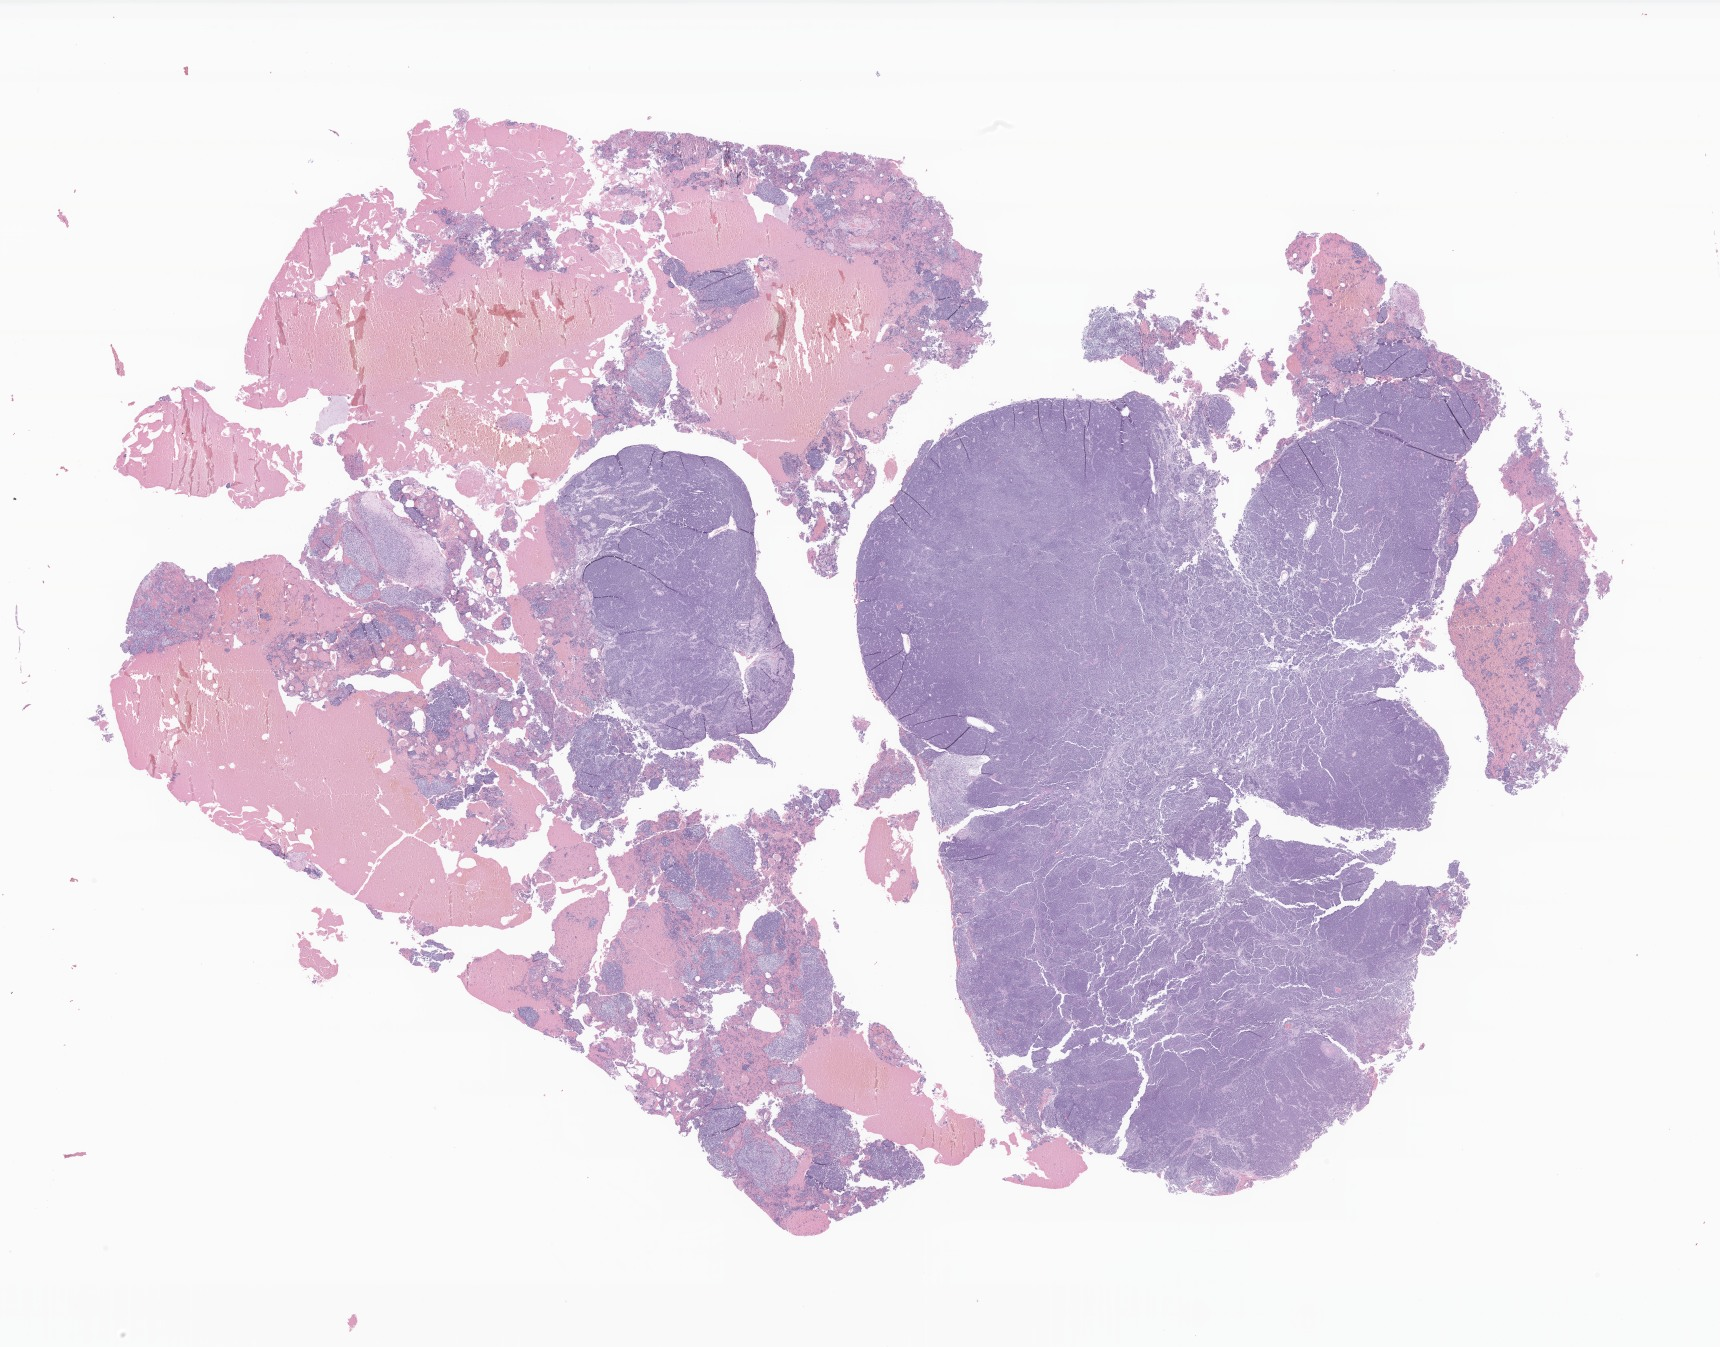
Haematoxylin and eosin whole-slide image of tumor tissue from the brain — low-resolution overview of the scanned area, about 29.0 x 22.7 mm, FFPE section. Male patient, age 75 months (6 years 3 months).
* recorded diagnosis: Medulloblastoma, NOS